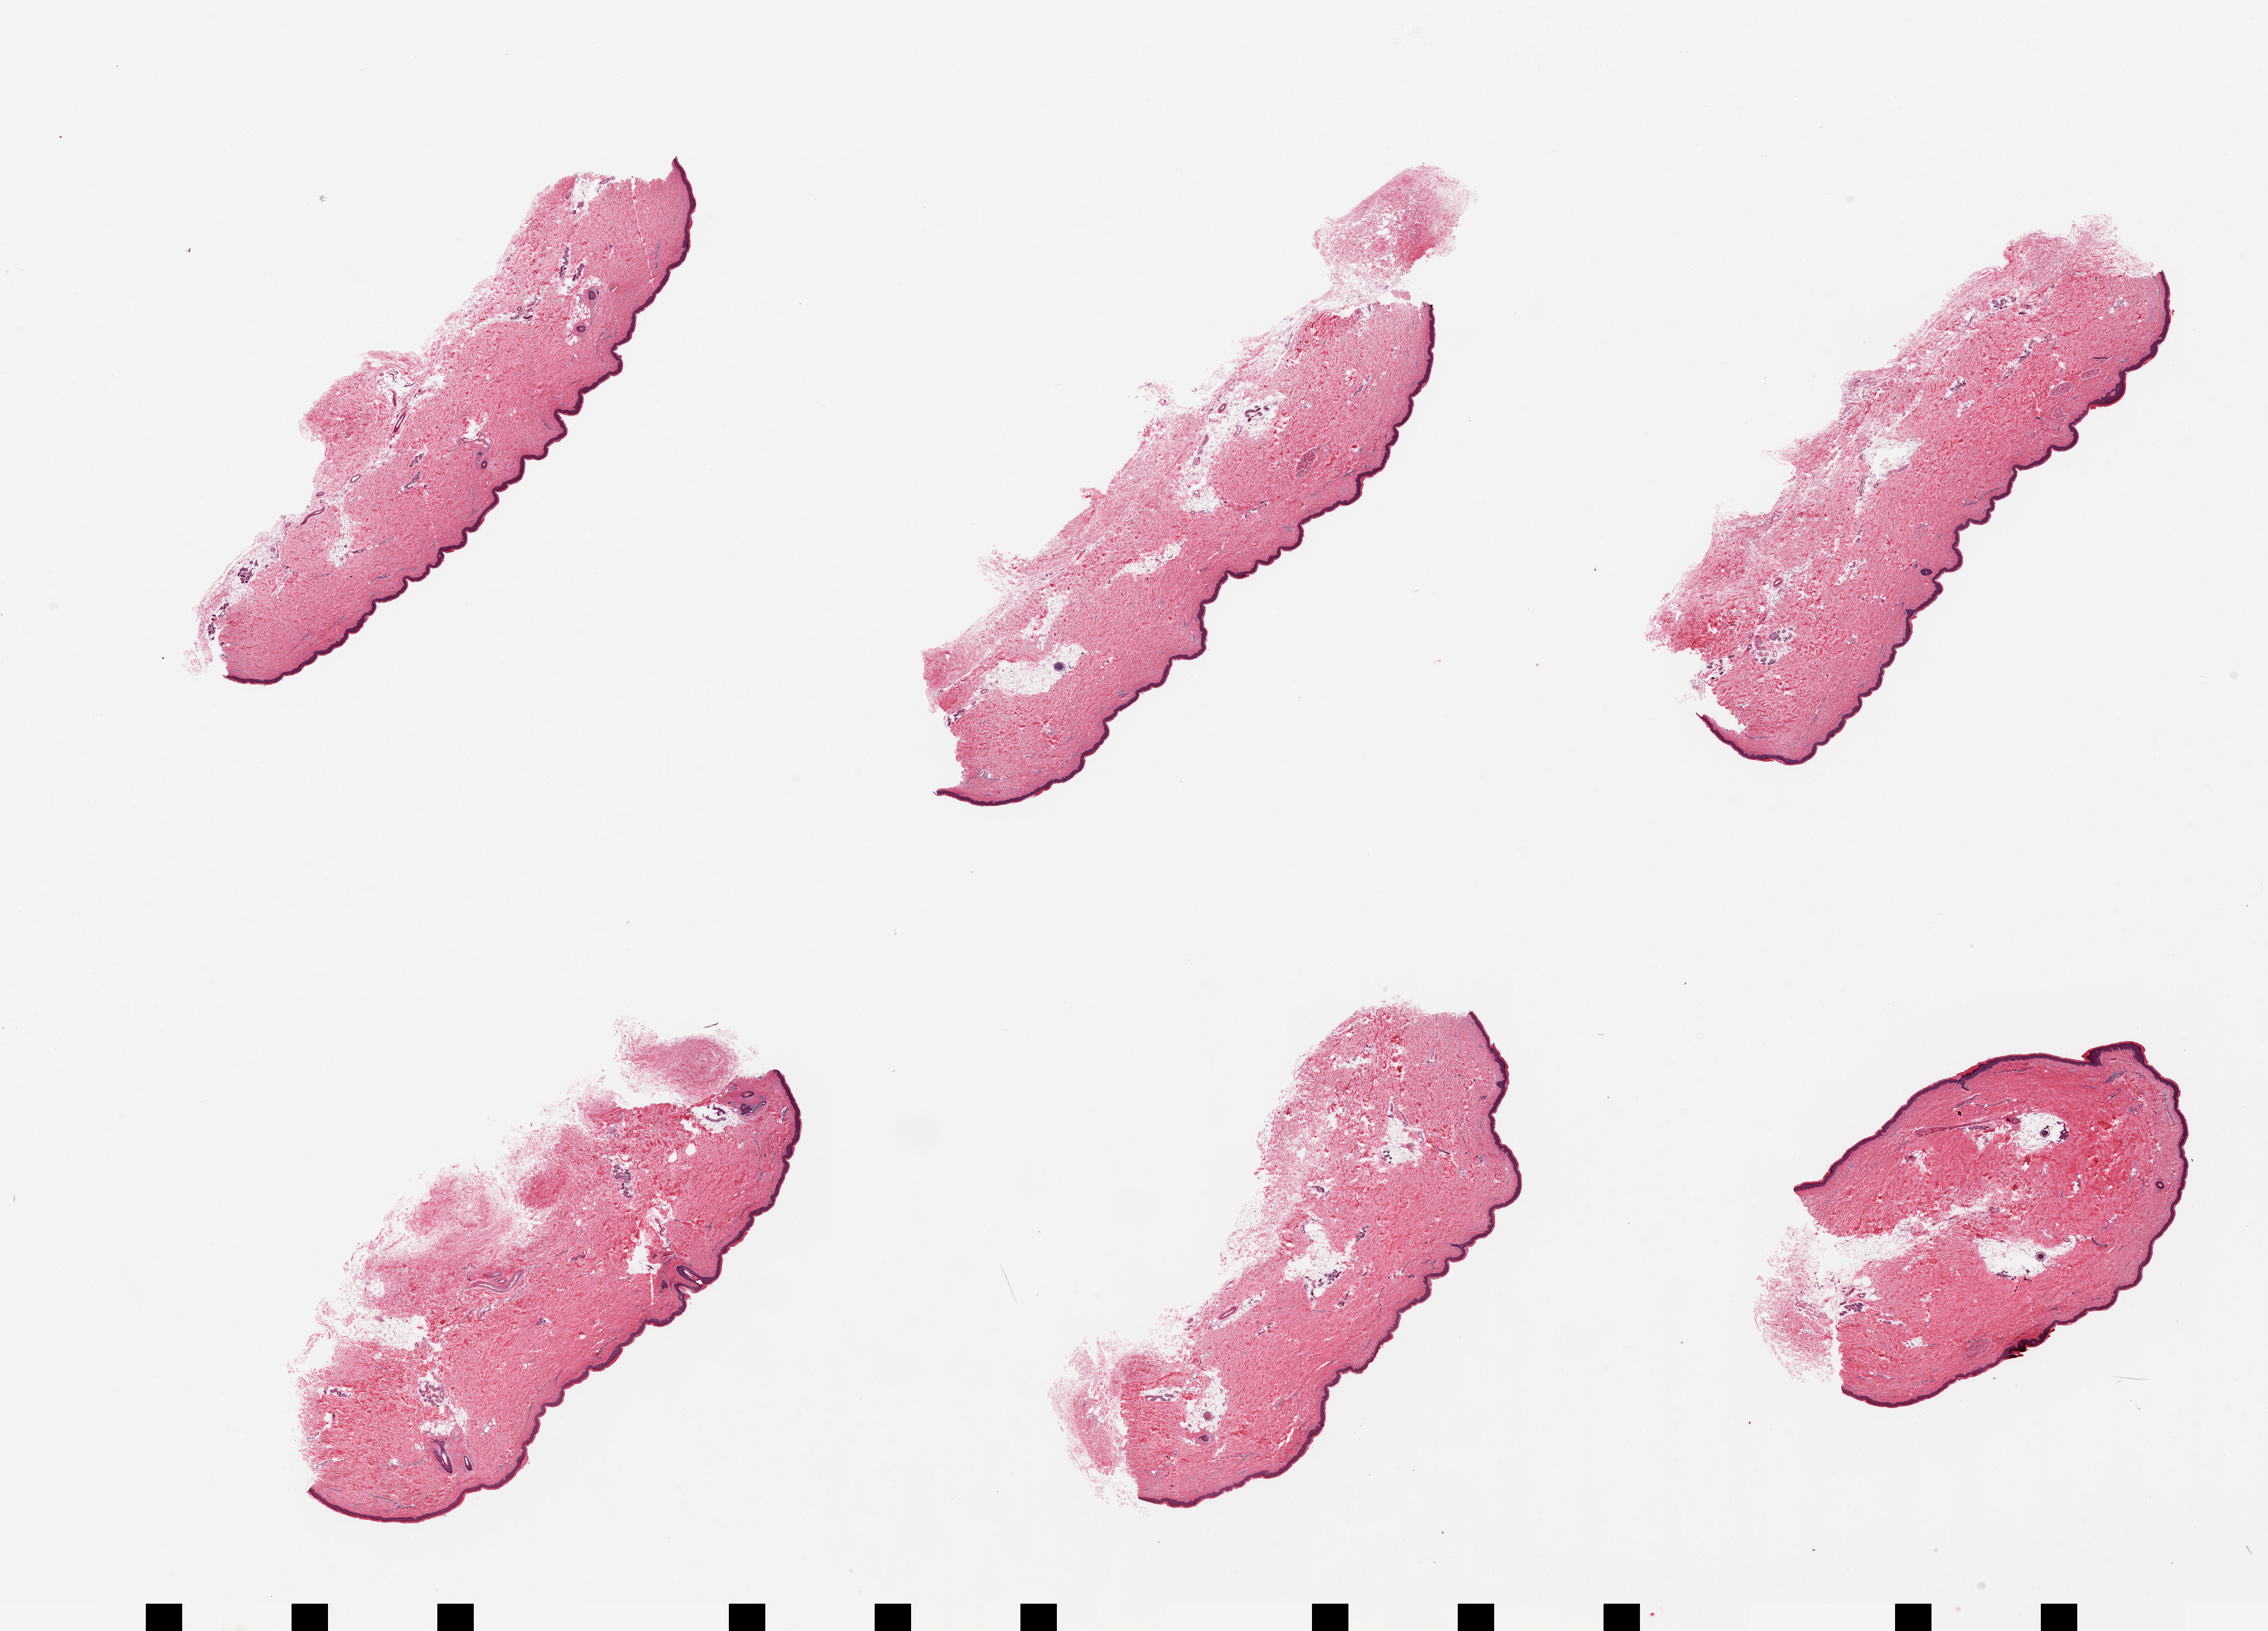
Hematoxylin and eosin (H&E) whole-slide image — whole scanned area (about 29.5 x 21.2 mm, from a 20x scan) shown as a low-resolution overview. PAXgene-fixed, paraffin-embedded tissue. Sampled site (target tissue): skin of lower leg. Donor tissue sample.
- review note (as recorded): 6 pieces, minimal attached fat, squamous epithelium is 40-50 microns thick